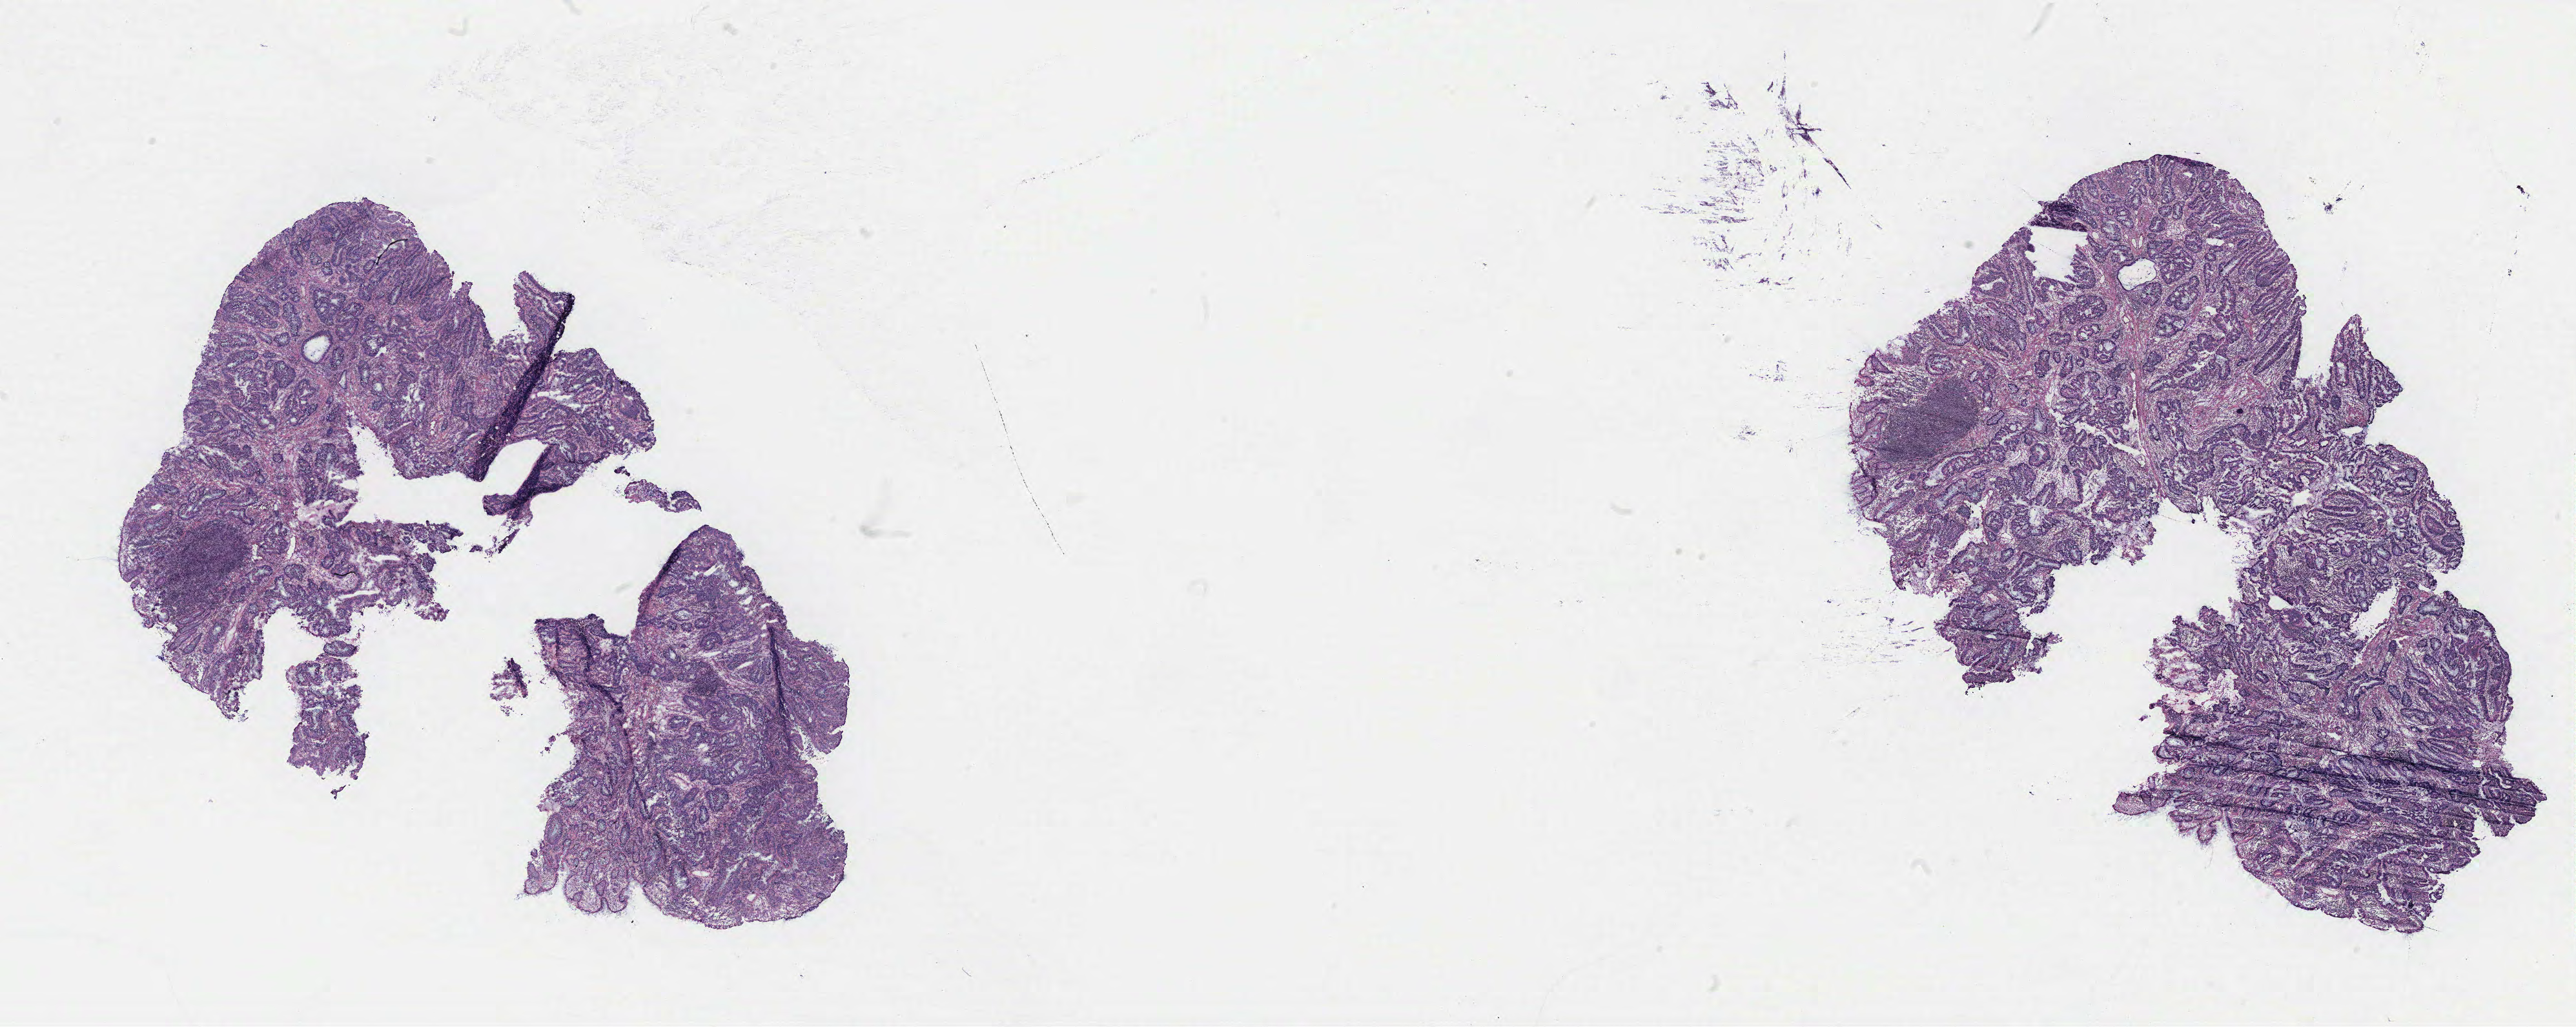
Digitized H&E tissue section (whole slide), shown as a low-resolution overview of the whole scanned area (about 31.9 x 12.7 mm); normal (non-tumour) tissue sample, colon. Patient: female, age 55 years.
* this section: normal (non-tumour) tissue from the same patient
* patient diagnosis: Adenocarcinoma, NOS